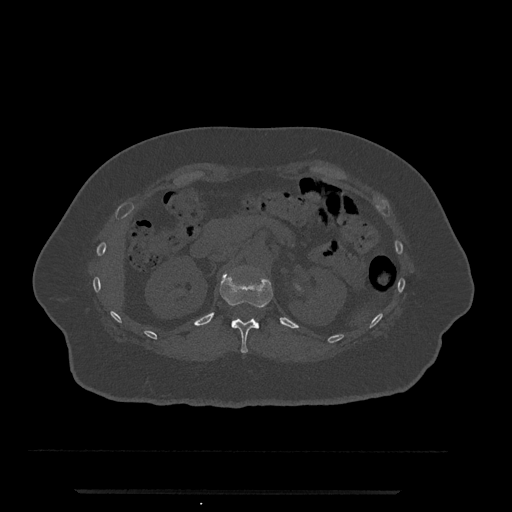
CT including the spine, one axial slice. Position 155 of 797 along the scan axis. Reconstruction kernel Br40s/3. 120 kVp. Bone window (W 1800 / L 400 HU). 0.5 mm slice thickness. 512 × 512 image matrix, field of view 440 × 440 mm. Patient: female, 51 years. From the clinical record (not read from this slice): primary cancer: neuro; vertebrae with lytic lesions (as recorded): T8.
Outlined on this slice (semi-automatically segmented with operator editing):
- T12 vertebra: bounding box [x1, y1, x2, y2] px = [219, 273, 273, 353]